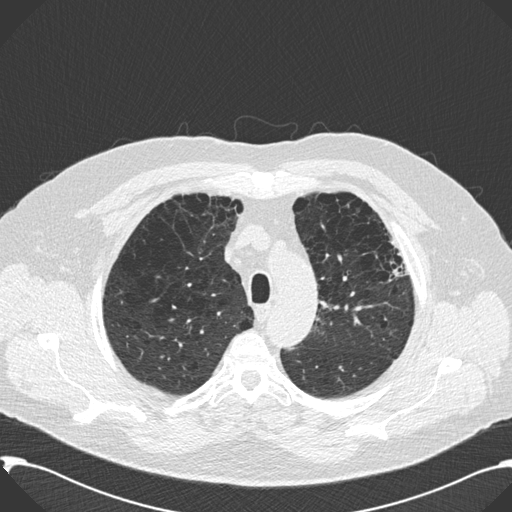
Chest CT (low-dose screening protocol), one axial image; second screening round (one year after baseline); lung window (W 1500 / L -600 HU); 2 mm slice thickness; standard (soft-tissue) reconstruction kernel (B30f). Male, age 59 years at enrolment.
- Expert-annotated lung lesion, bounding box (x1, y1, x2, y2) in pixels: (365, 229, 415, 301).
- Screening reader's record for this exam: no non-calcified nodule ≥4 mm recorded.